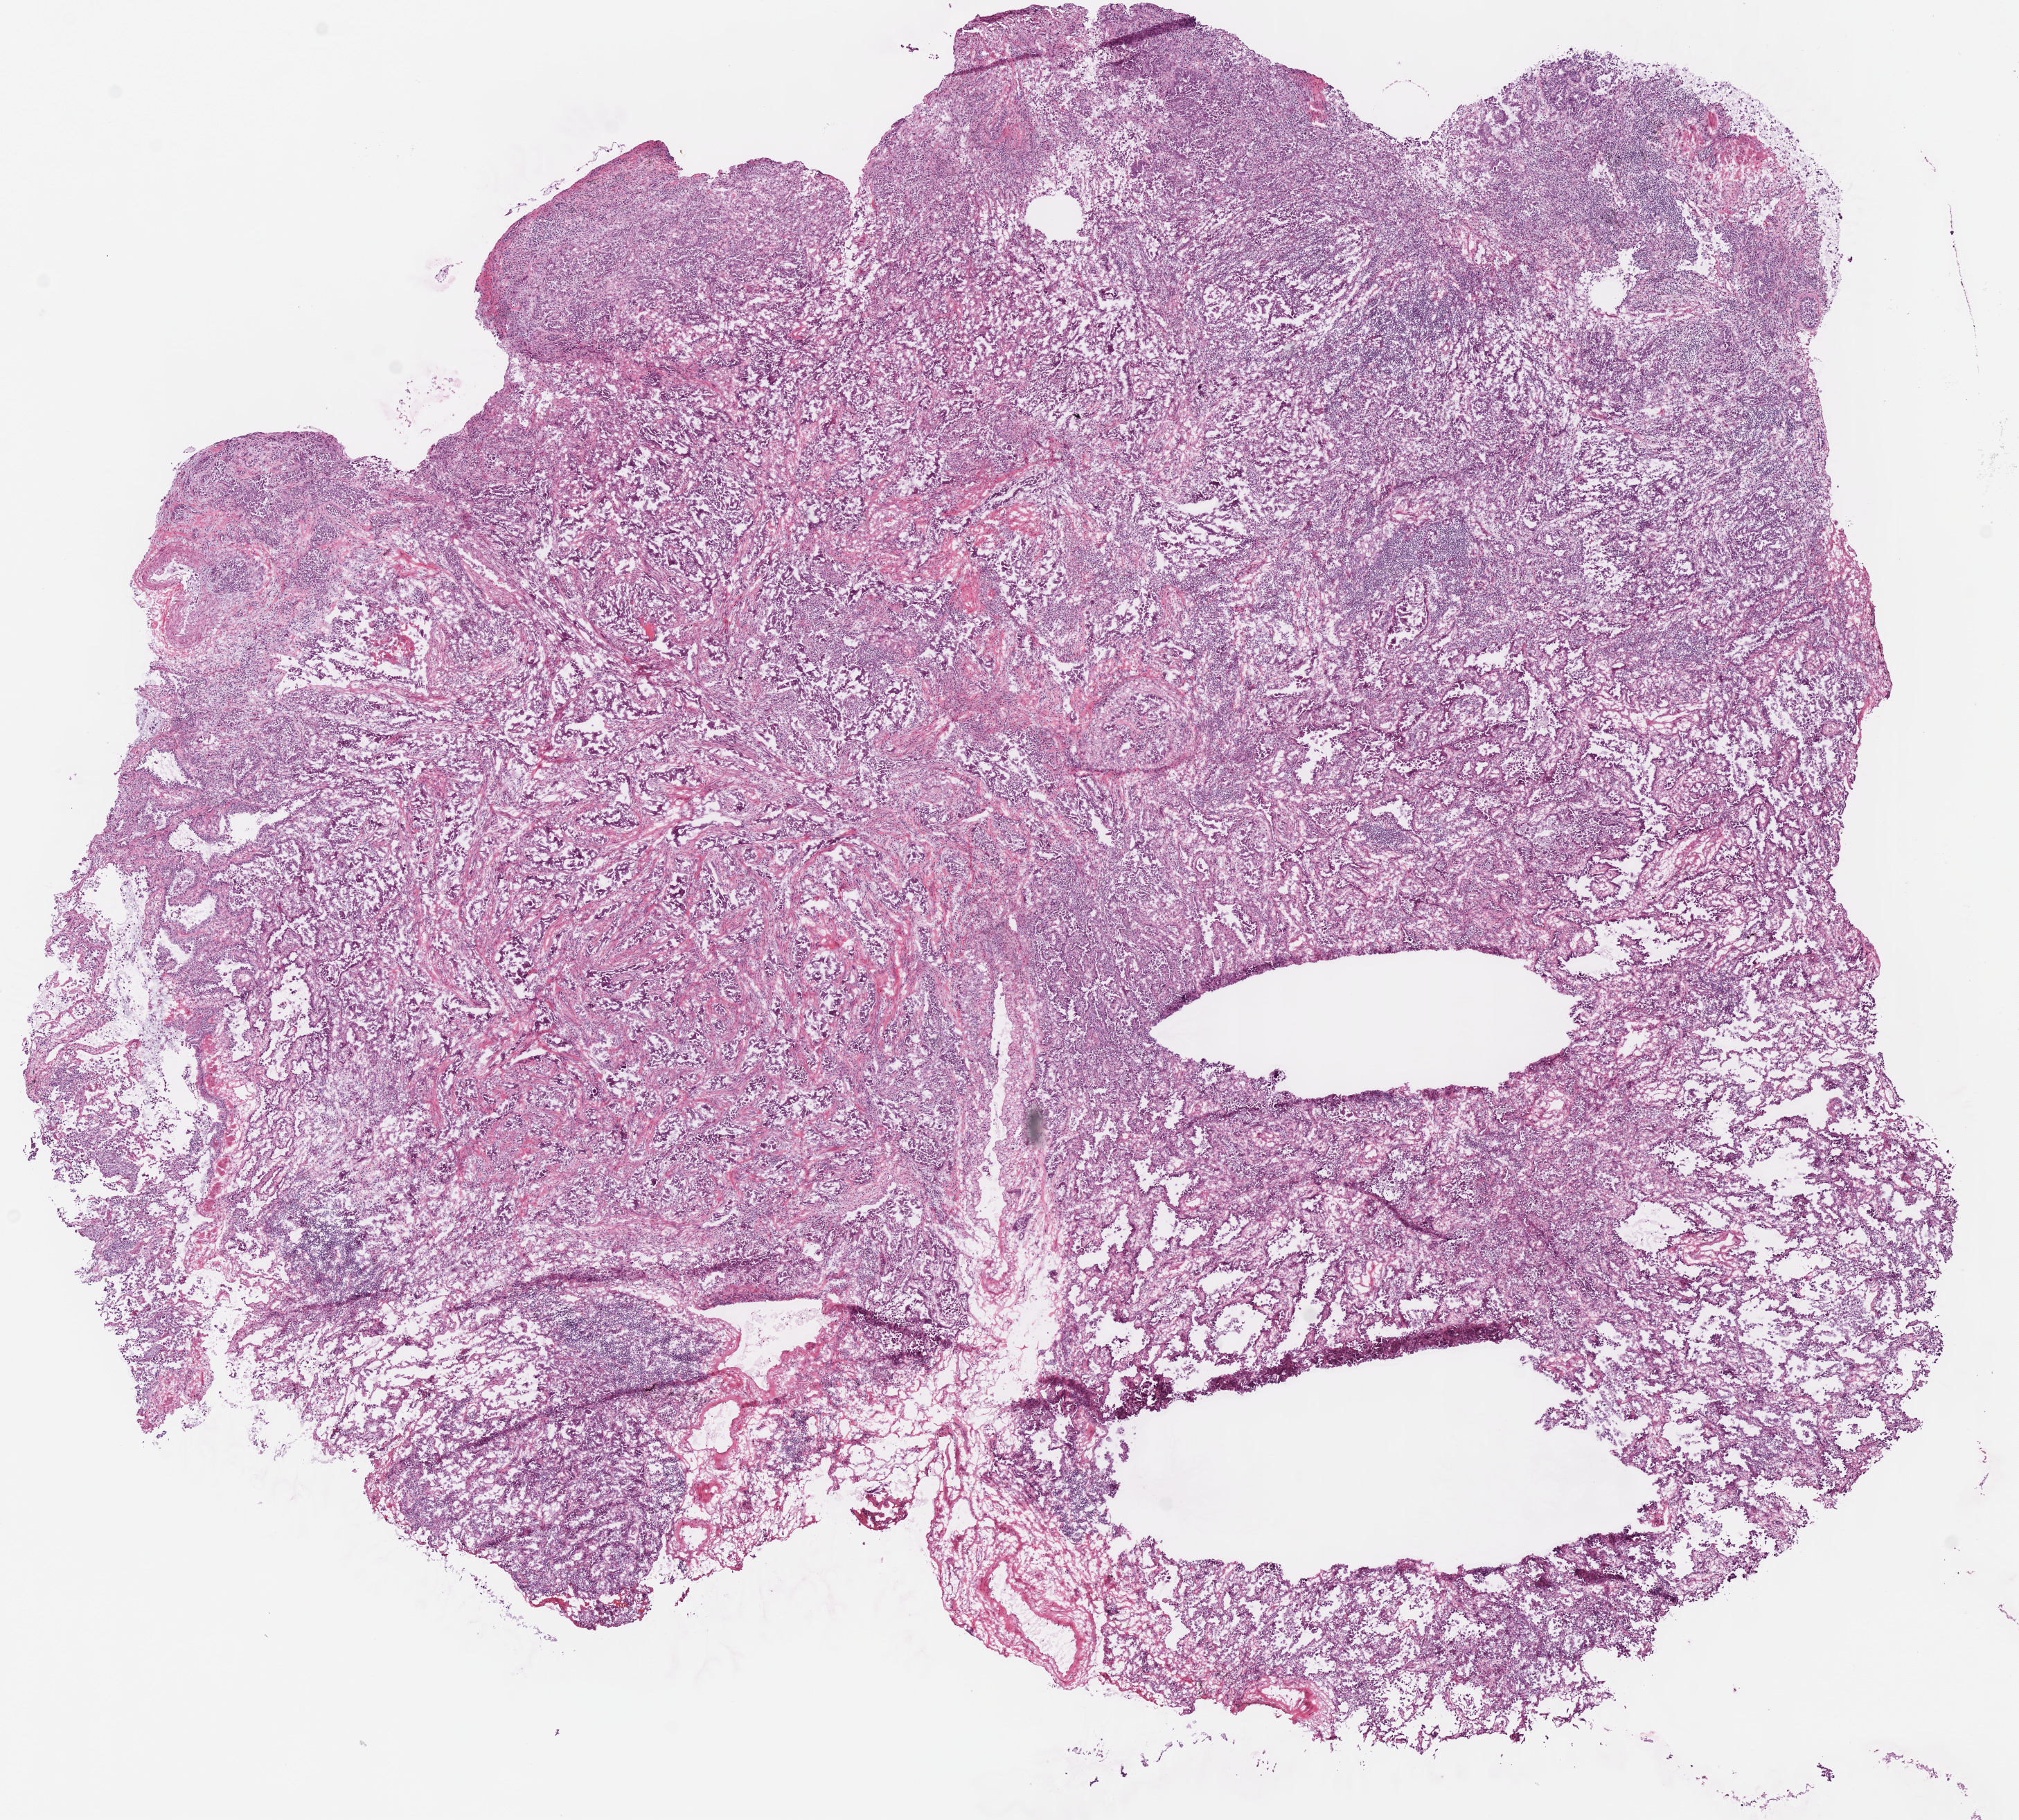
Whole-slide histology image, Hematoxylin and eosin (H&E) stained — shown as a low-resolution overview of the whole scanned area (about 11.5 x 10.4 mm, from a 40x scan). Frozen section from the bottom of the tissue portion. Lung, primary tumour sample. Female patient; age at initial diagnosis 76 years. Slide review estimates, as recorded: tumour cells 80%, tumour nuclei 60%, normal cells 5%, stromal cells 15%, necrosis 0%. Inflammatory infiltration, as recorded: lymphocyte infiltration 25%.
Pathologic diagnosis: Adenocarcinoma with mixed subtypes. TNM: T1a N0 MX. AJCC pathologic stage: IA.